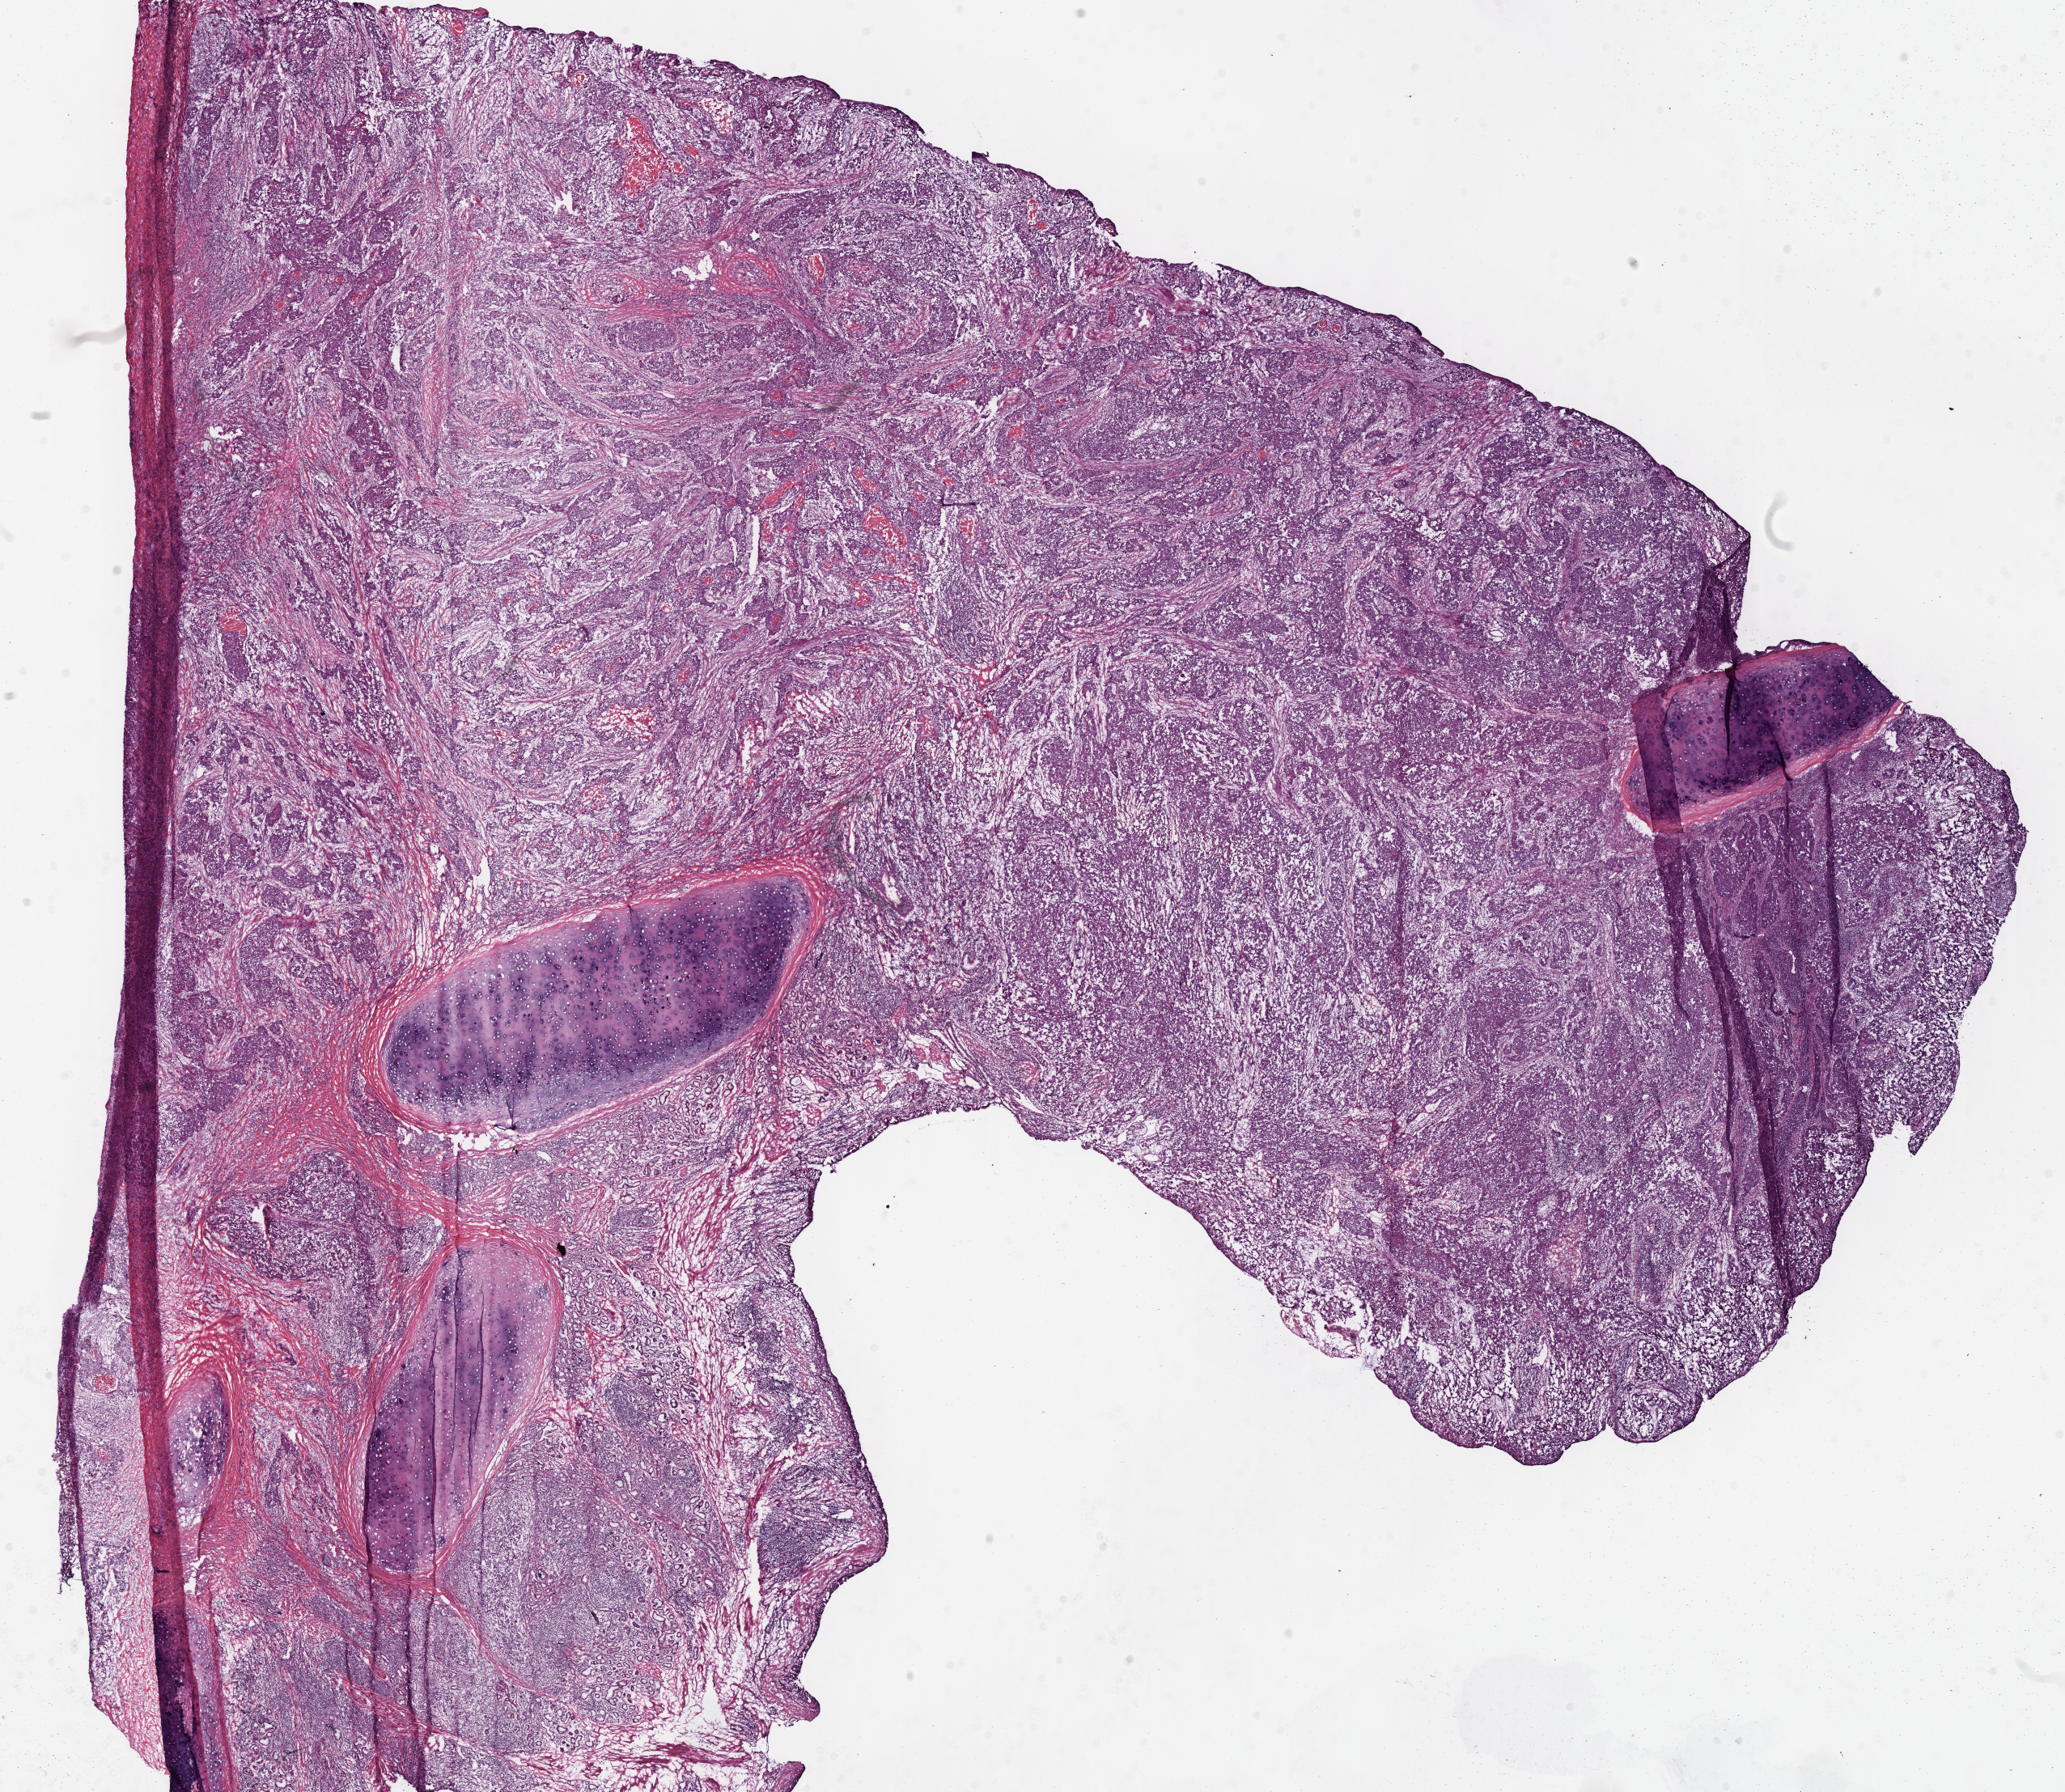
Digitized Hematoxylin and eosin (H&E) stained tissue section (whole slide), shown as a low-resolution overview of the whole scanned area (about 20.1 x 17.4 mm, slide scanned at 40x). Frozen section from the top of the tissue portion. Sample: primary tumour, lung. Male patient; age at initial diagnosis 57 years. Pathologist review of this section (percent, as recorded): tumour cells 65%, tumour nuclei 60%, normal cells 20%, stromal cells 13%, necrosis 2%. Infiltration values recorded for this section: lymphocyte infiltration 25%, monocyte infiltration 1%.
Pathologic diagnosis: Squamous cell carcinoma, NOS (lower lobe, lung). AJCC pathologic stage: IB (7th edition).